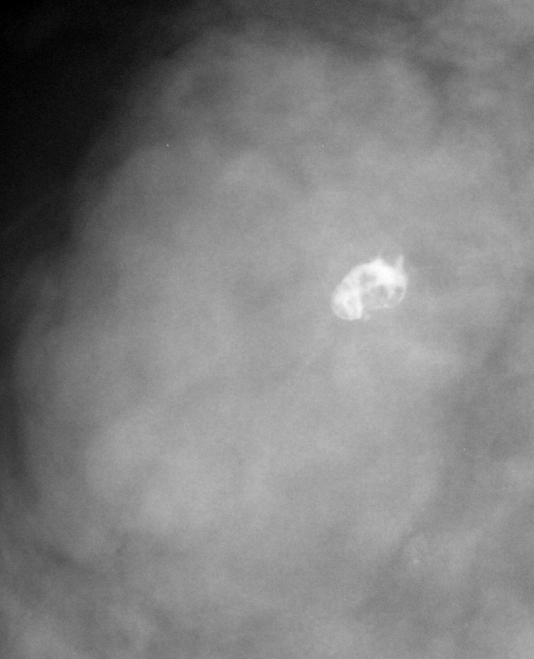
Region of interest cut from a scanned film mammogram (one marked finding), right breast, MLO view.
Finding: mass, shape lobulated, margins microlobulated; BI-RADS assessment category 4; subtlety rating 5 on a 1 (subtle) to 5 (obvious) scale; pathology (as recorded): benign.